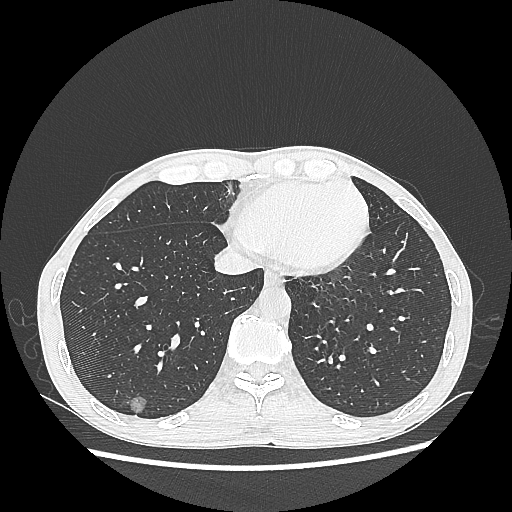
Chest CT, one axial slice. Slice 78 of 270 in the series (ordered by position). Reconstruction kernel LUNG. 100 kVp. Lung window (W 1500 / L -600 HU). 1.25 mm slice thickness. 512 × 512 image matrix, field of view 360 × 360 mm. Patient: male, 60 years. Case-level facts recorded for this patient, not image findings: clinical TNM (as recorded): T1c N0 M0; histopathological grade: G2.
Outlined on this slice (rectangle marked by the reading radiologist):
- lung tumour (recorded histology: adenocarcinoma): bounding box <122,389,148,417> (left, top, right, bottom; pixels)